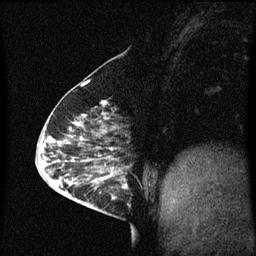
Breast MRI (dynamic contrast-enhanced), one sagittal slice; position 24 of 60 along the scan axis; dynamic contrast-enhanced series, image 2 of 3 at this slice position (ordered by acquisition); 1.5 T; TE 4.2 ms, TR 8.4 ms; 2 mm slice thickness; 256 × 256 image matrix, field of view 200 × 200 mm. Female patient, age 63 years.
Outlined on this slice (semi-automatic segmentation, software-assisted and operator-edited):
- analysis volume of interest (the breast-tissue region the enhancement analysis was run in; not a lesion): bounding box <98,168,133,217> (left, top, right, bottom; pixels)
- tumour enhancement mask (voxels above the 70 % enhancement threshold inside the analysis volume of interest): <100,168,127,199>